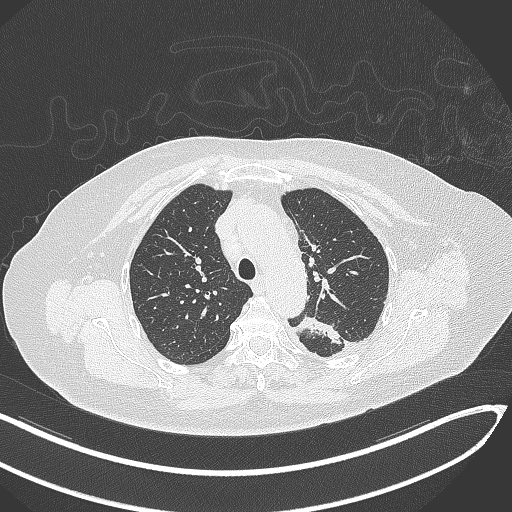
Chest CT, one axial slice; position 232 of 270 along the scan axis; 120 kVp; lung window (W 1500 / L -600 HU); 512 × 512 image matrix, field of view 400 × 400 mm. Patient: female, 76 years. From the clinical record (not read from this slice): clinical TNM (as recorded): T1c N0 M0.
Annotated regions visible in this slice (rectangle marked by the reading radiologist):
- lung tumour (recorded histology: adenocarcinoma): box from (x=293, y=316) to (x=345, y=348) px